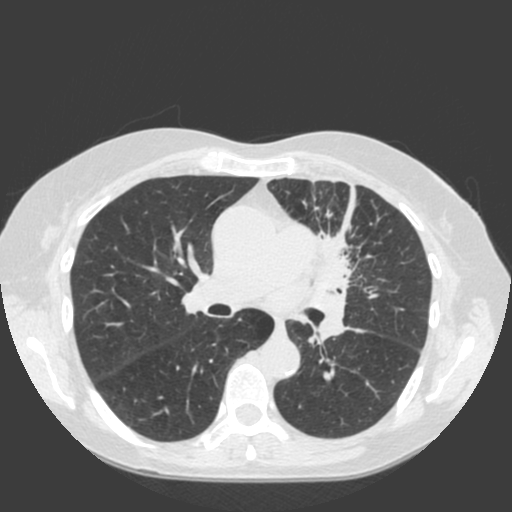
Low-dose screening chest CT, one axial slice. Position 112 of 184 along the scan axis. Lung window (W 1500 / L -600 HU). 512 × 512 image matrix, field of view 350 × 350 mm.
Annotated regions visible in this slice (expert manual segmentation):
- lesion 1 (tumor, hilum of left lung): box from (x=305, y=231) to (x=353, y=344) px